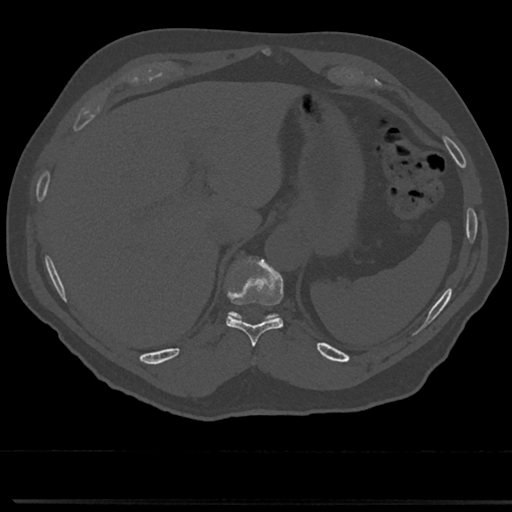
CT including the spine, one axial slice; position 245 of 817 along the scan axis; reconstruction kernel Br40s/3; 120 kVp; bone window (W 1800 / L 400 HU); 0.5 mm slice thickness; 512 × 512 image matrix, field of view 355 × 355 mm. Male patient, age 61 years. Case-level facts recorded for this patient, not image findings: primary cancer: prostate.
Annotated regions visible in this slice (semi-automatic segmentation, software-assisted and operator-edited):
- T10 vertebra: bounding box (x1, y1, x2, y2) in pixels: (223, 257, 285, 344)
- T11 vertebra: (232, 314, 240, 319)
- T9 vertebra: (252, 355, 257, 361)